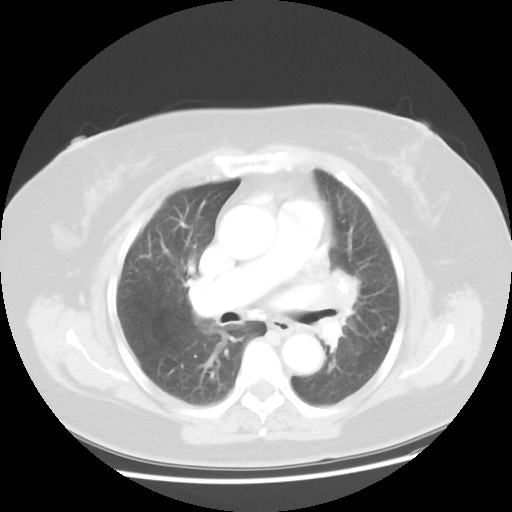
Chest CT, one axial slice; slice 26 of 49 in the series (ordered by position); reconstruction kernel STANDARD; lung window (W 1500 / L -600 HU); 5 mm slice thickness; 512 × 512 image matrix, field of view 374 × 374 mm. Patient: female, 58 years. Case-level facts recorded for this patient, not image findings: clinical TNM (as recorded): T4 N3 M0; histopathological grade: G3.
Outlined on this slice (rectangle marked by the reading radiologist):
- lung tumour (recorded histology: small cell carcinoma): box from (x=307, y=256) to (x=381, y=370) px